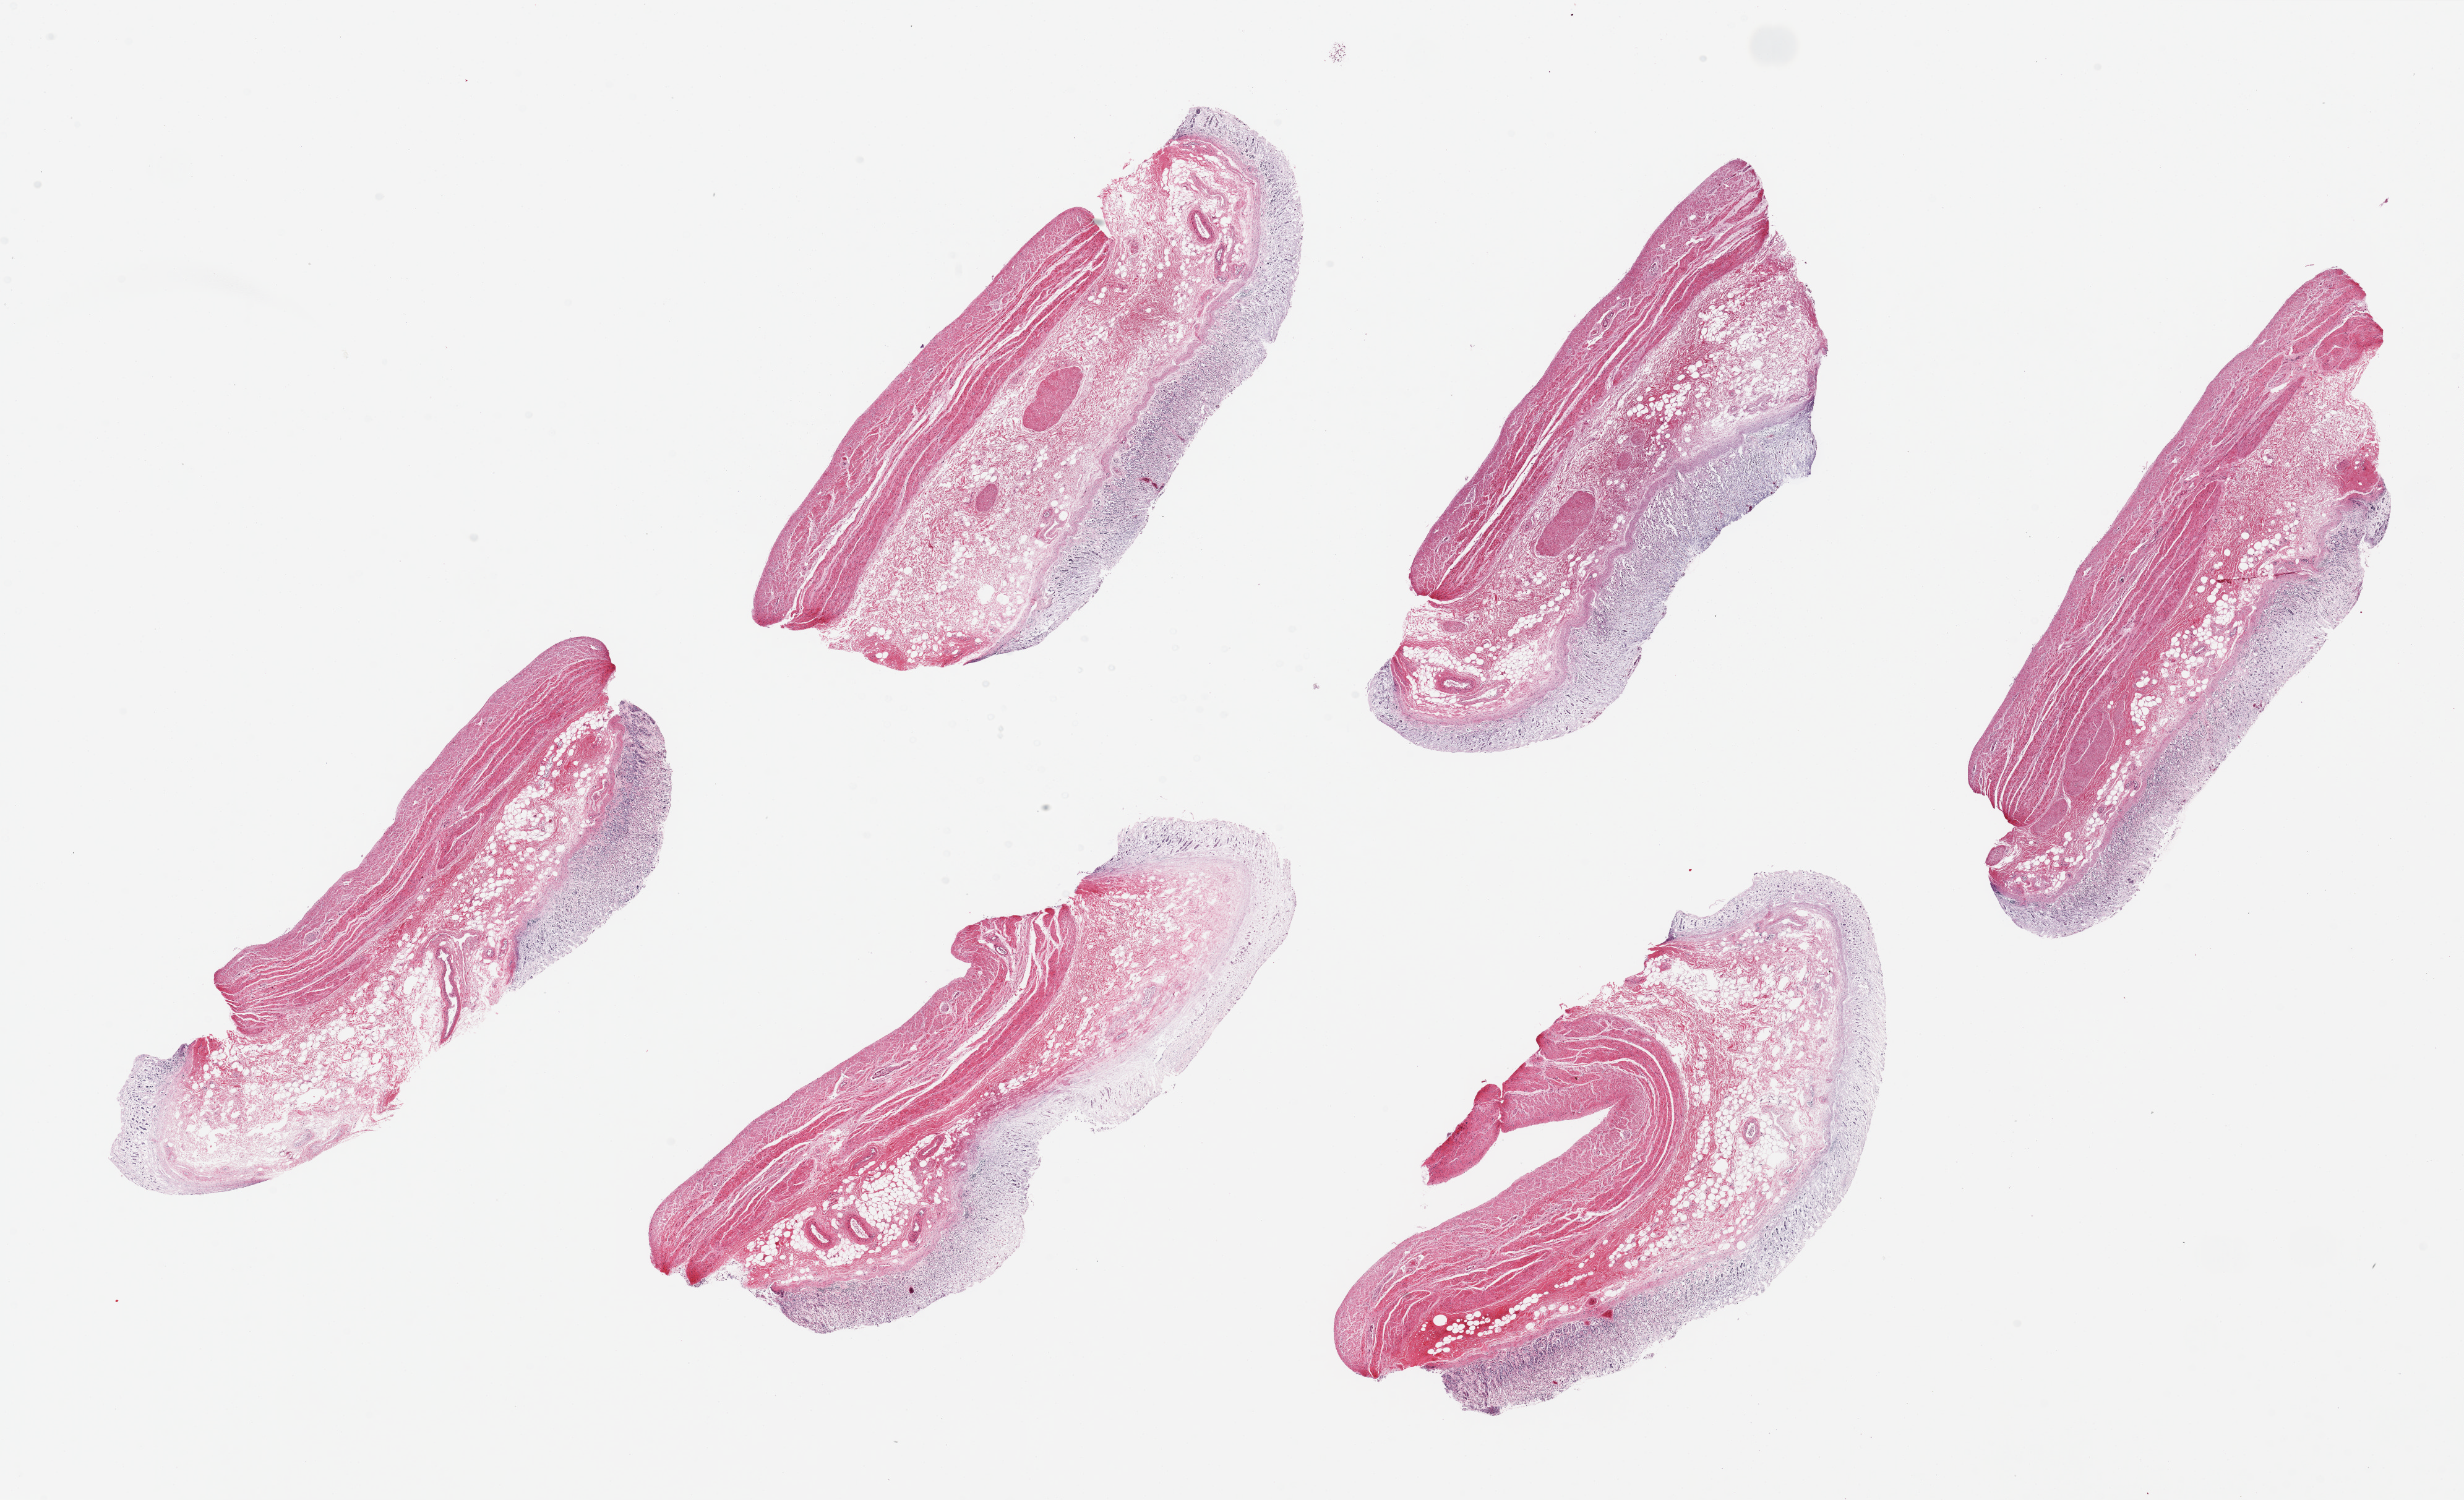
Digitized hematoxylin and eosin (H&E)-stained section, whole scanned area (about 31.5 x 19.2 mm) shown as a low-resolution overview, PAXgene-fixed paraffin-embedded (PFPE) section, sampled site (target tissue): stomach, donor tissue sample. Donor sex: male.
Reviewer comment on this tissue sample: 6 pieces ~8x3mm, mucosa ~25% thickness but all autolyzed/sloughing.